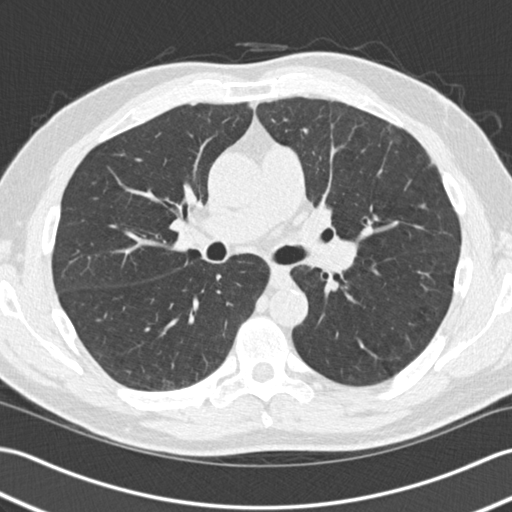
Low-dose screening chest CT, one axial slice. Slice 77 of 140 in the series (ordered by position). 120 kVp. Lung window (W 1500 / L -600 HU). 2 mm slice thickness. 512 × 512 image matrix, field of view 352 × 352 mm.
Annotated regions visible in this slice (manually delineated by an expert):
- lesion 1 (tumor, upper lobe of left lung): bounding box (x1, y1, x2, y2) in pixels: (431, 161, 436, 166)